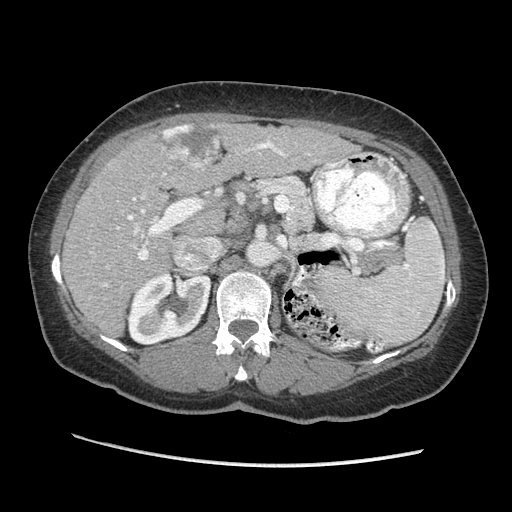
Contrast-enhanced abdominal CT (liver protocol), one axial slice; position 126 of 170 along the scan axis; reconstruction kernel STANDARD; soft-tissue window (W 400 / L 40 HU); 512 × 512 image matrix. Case-level facts recorded for this patient, not image findings: diagnosis: hepatocellular carcinoma (patient treated with transarterial chemoembolisation; whether this scan precedes or follows treatment is not stated here); TNM stage (as recorded): Stage-II; Child-Pugh class: A; tumour differentiation: no biopsy; tumour nodularity: multinodular.
Annotated regions visible in this slice (semi-automatic segmentation, software-assisted and operator-edited):
- liver parenchyma outside the tumour (the mass and vessels are separate outlines, so this box may not span the whole liver): box from (x=62, y=122) to (x=358, y=336) px
- mass: (x=159, y=123)–(x=221, y=170)
- liver vessels: (x=104, y=141)–(x=310, y=287)